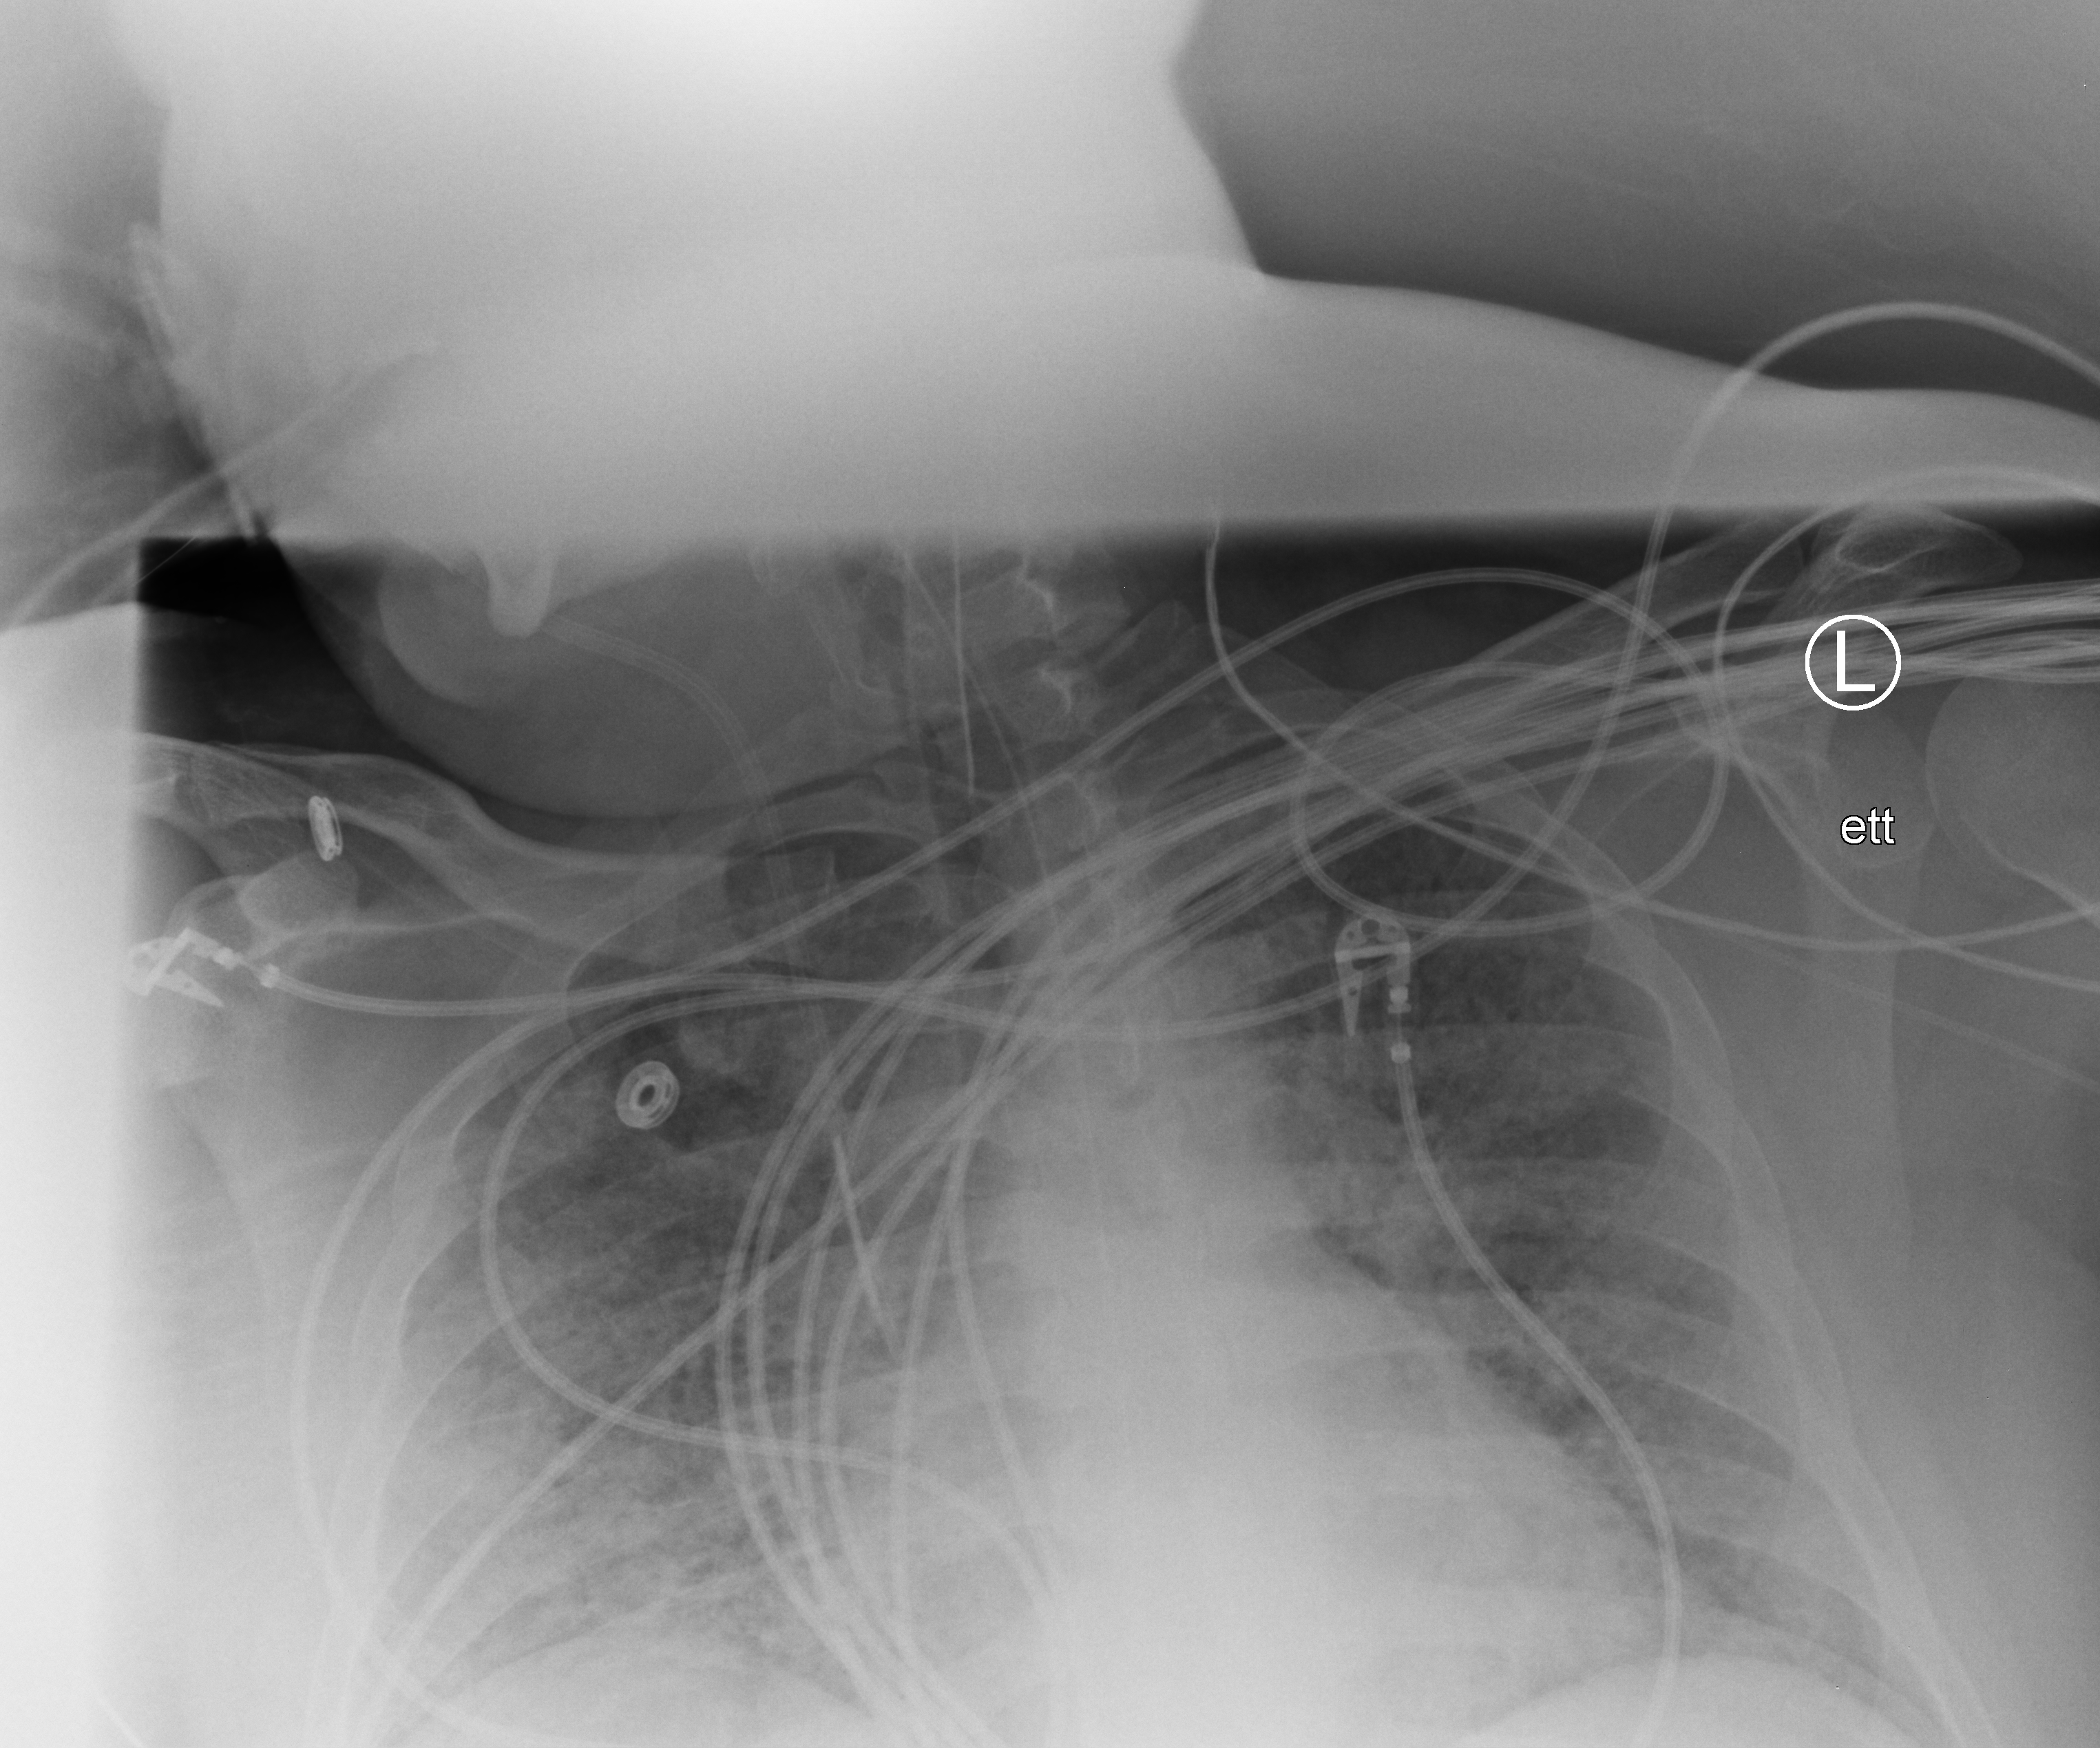
Portable chest radiograph, anteroposterior (AP) projection. Patient hospitalised with COVID-19, aged 18–59 years.
From the hospital-stay record, not from the radiograph (when in the stay this image was taken is not recorded):
- length of hospital stay: 22 days